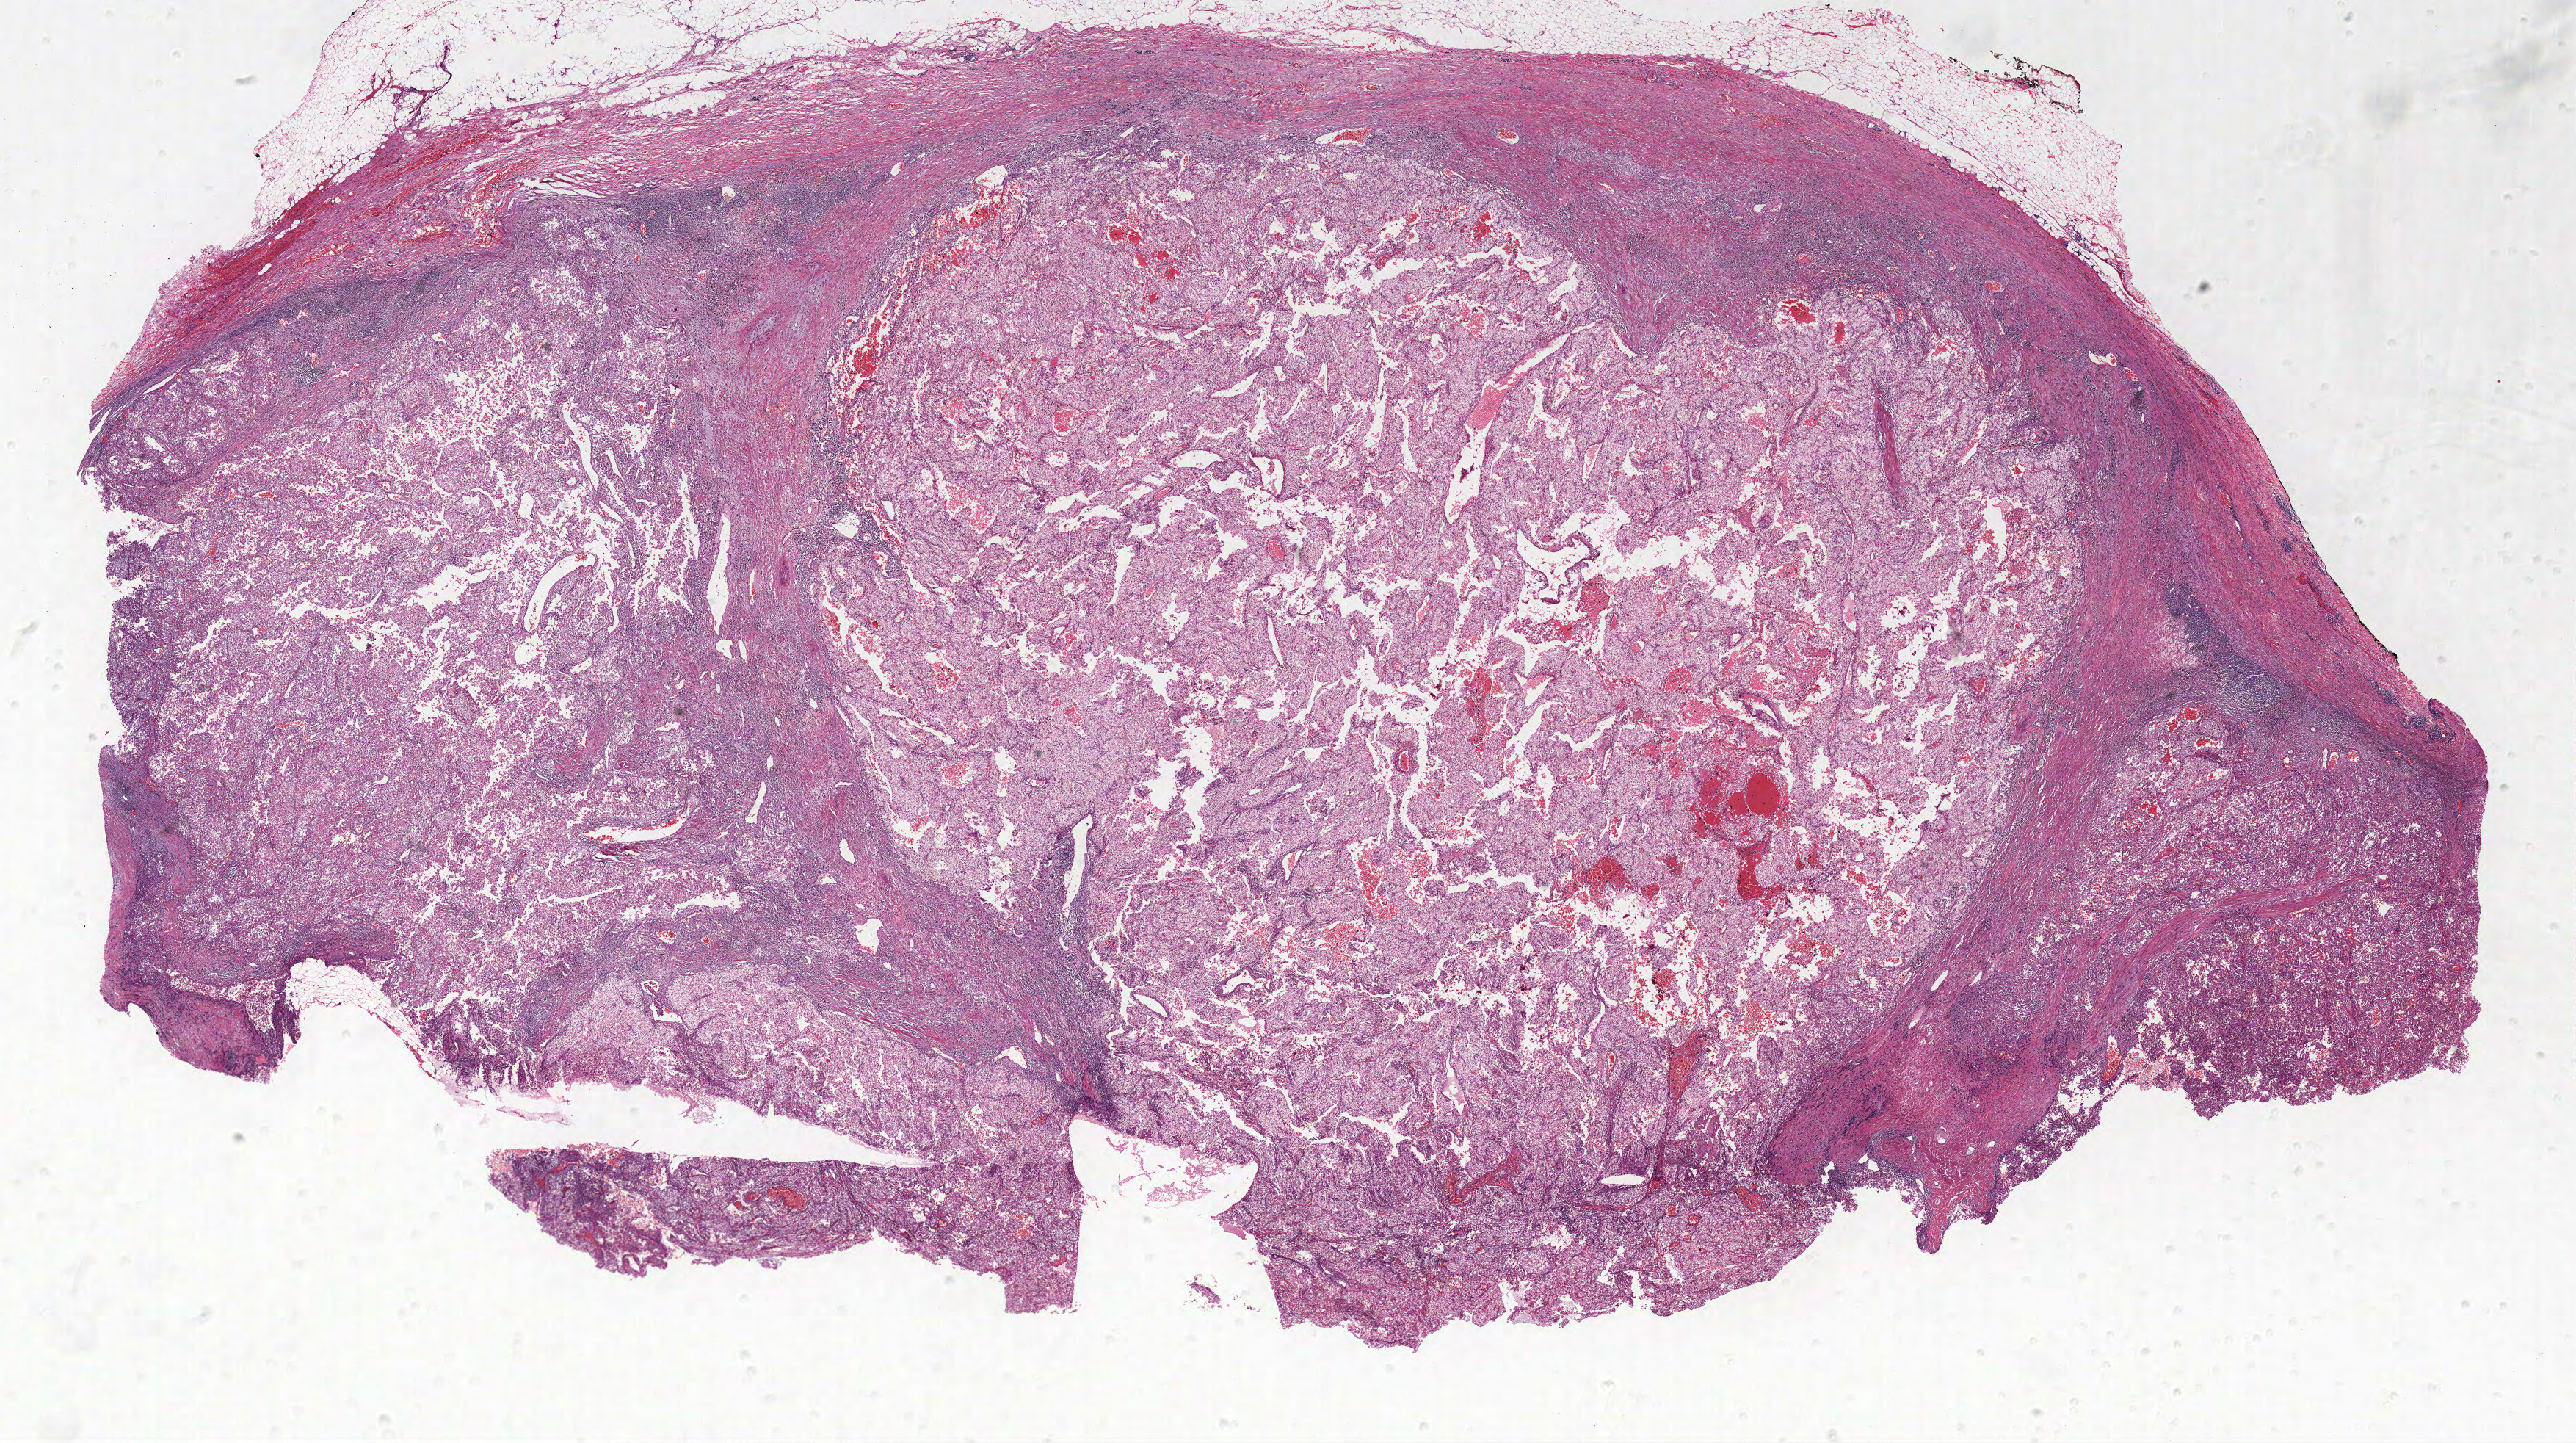
H&E whole-slide image — low-resolution overview of the scanned area, about 28.1 x 15.7 mm; FFPE section; primary tumour sample from the kidney. Patient: male, age at initial diagnosis 43 years. Histologic grade: G3 (poorly differentiated).
• histologic diagnosis: Clear cell adenocarcinoma, NOS
• AJCC pathologic stage: I